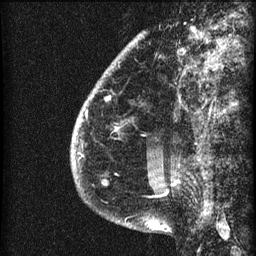
Breast MRI (dynamic contrast-enhanced), one sagittal slice. 3 images stored at this slice position (order not interpretable as contrast timing). 1.5 T. TE 4.2 ms, TR 22.7 ms. 2 mm slice thickness. 256 × 256 image matrix, field of view 180 × 180 mm. Female patient, age 48 years. Case-level facts recorded for this patient, not image findings: setting: breast cancer imaged before/during neoadjuvant chemotherapy; receptor status: triple-negative.
Structures marked on this image (semi-automatically segmented with operator editing):
- analysis volume of interest (the breast-tissue region the enhancement analysis was run in; not a lesion): bounding box [x1, y1, x2, y2] px = [71, 32, 173, 207]
- tumour enhancement mask (voxels above the 90 % enhancement threshold inside the analysis volume of interest): [76, 157, 79, 163]